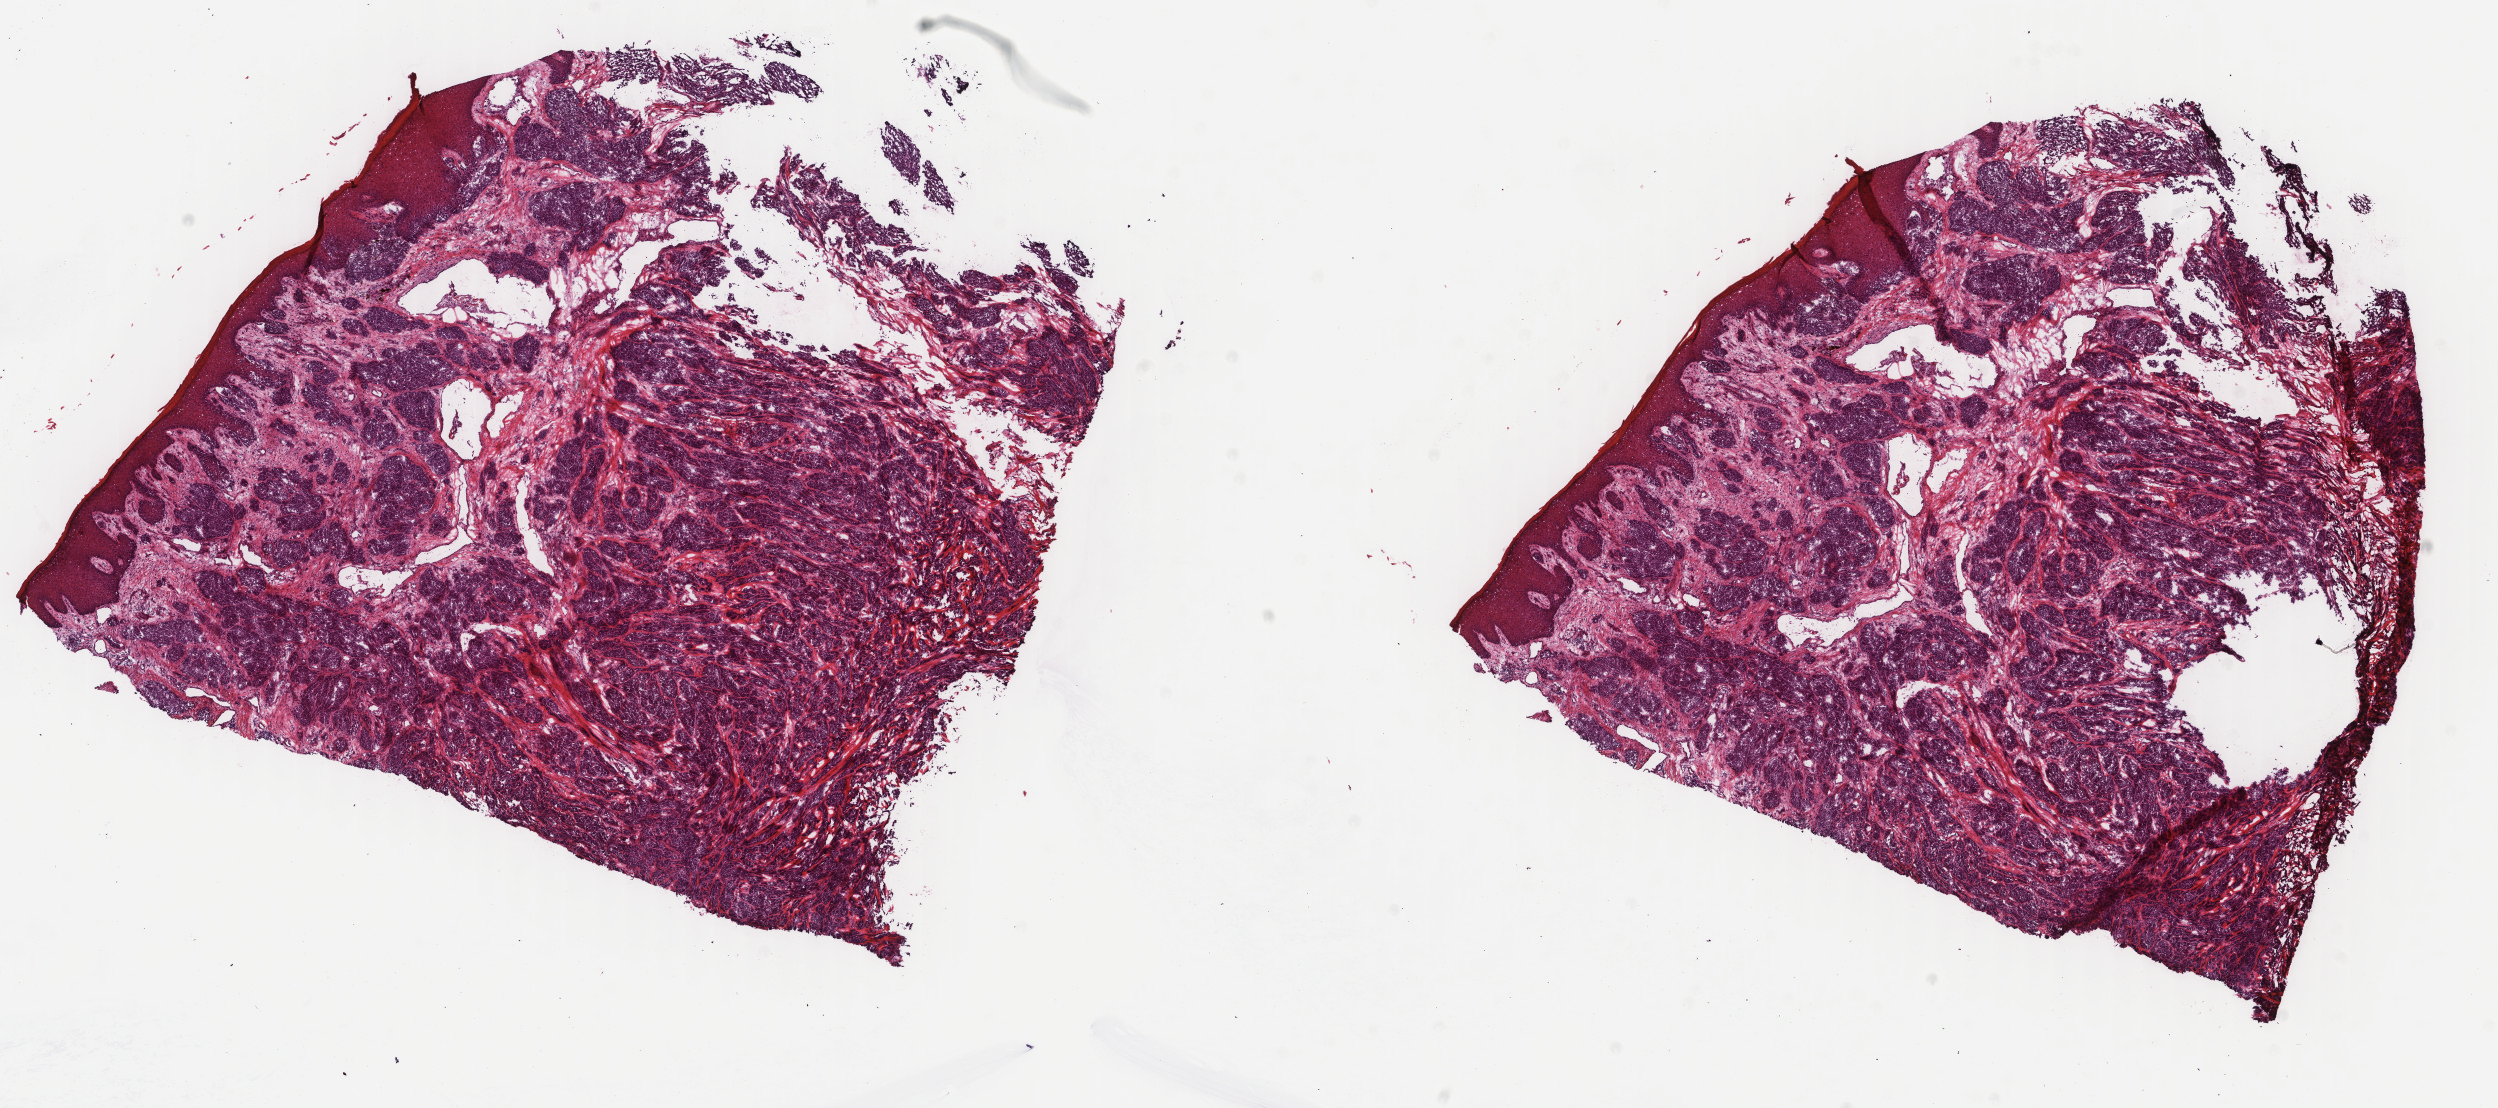
Whole-slide histology image, H&E-stained — a low-resolution overview of the entire scanned area, about 19.8 x 8.8 mm (from a 40x scan). Frozen section from the top of the tissue portion. Sample: primary tumour, skin. Patient: male, age at initial diagnosis 56 years. Composition of this section per pathologist review: tumour cells 95%, tumour nuclei 90%, normal cells 5%, stromal cells 0%, necrosis 0%. Infiltration values recorded for this section: lymphocyte infiltration 0%, monocyte infiltration 0%, neutrophil infiltration 0%.
Histologic diagnosis: Malignant melanoma, NOS.